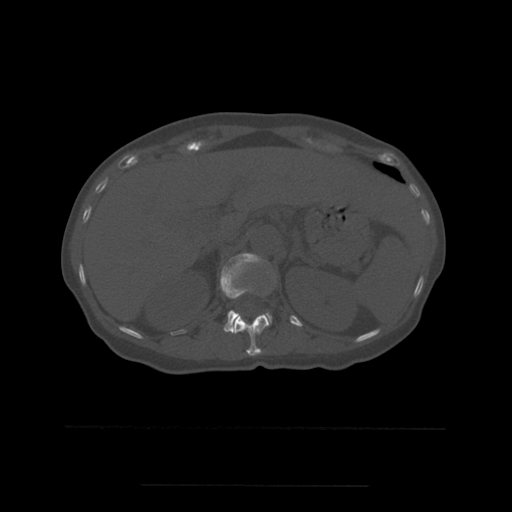
CT including the spine, one axial slice. Slice 248 of 544 in the series (ordered by position). Bone window (W 1800 / L 400 HU). 1.25 mm slice thickness. 512 × 512 image matrix, field of view 350 × 350 mm. Patient age 58 years. From the clinical record (not read from this slice): primary cancer: lung.
Annotated regions visible in this slice (semi-automatically segmented with operator editing):
- L1 vertebra: box from (x=220, y=253) to (x=273, y=333) px
- T12 vertebra: (x=233, y=315)–(x=270, y=356)